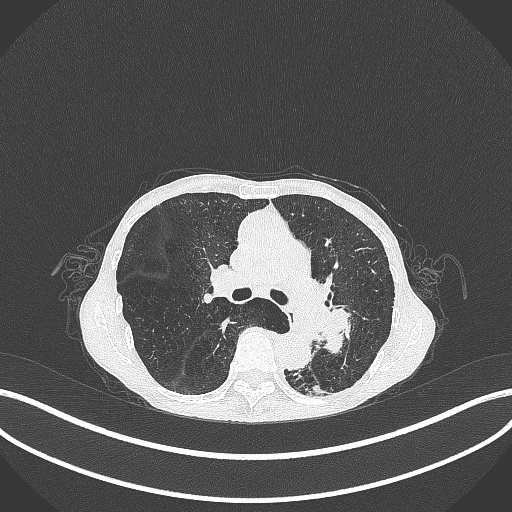
Chest CT, one axial slice; slice 171 of 347 in the series (ordered by position); lung window (W 1500 / L -600 HU); 1 mm slice thickness; 512 × 512 image matrix. Female patient, age 70 years. From the clinical record (not read from this slice): clinical TNM (as recorded): T3 N0 M0; histopathological grade: G3.
Outlined on this slice (bounding box drawn by a radiologist):
- lung tumour (recorded histology: small cell carcinoma): bounding box [x1, y1, x2, y2] px = [318, 300, 355, 361]